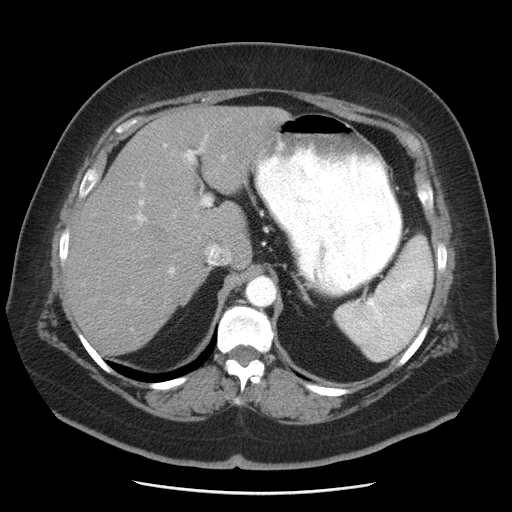
Contrast-enhanced abdominal CT, one axial slice. Position 33 of 55 along the scan axis. Intravenous contrast given. Soft-tissue window (W 400 / L 40 HU). 5 mm slice thickness. 512 × 512 image matrix, field of view 380 × 380 mm. Female patient, age 52 years. From the clinical record (not read from this slice): diagnosis: colorectal cancer liver metastases, imaged before liver resection; multiple liver metastases: yes; largest metastasis: 2.5 cm.
Structures marked on this image (expert manual segmentation):
- liver: bounding box (x1, y1, x2, y2) in pixels: (66, 106, 292, 356)
- planned liver remnant (the part of the liver to remain after resection): (66, 177, 208, 356)
- portal vein (with intrahepatic branches): (128, 137, 226, 300)